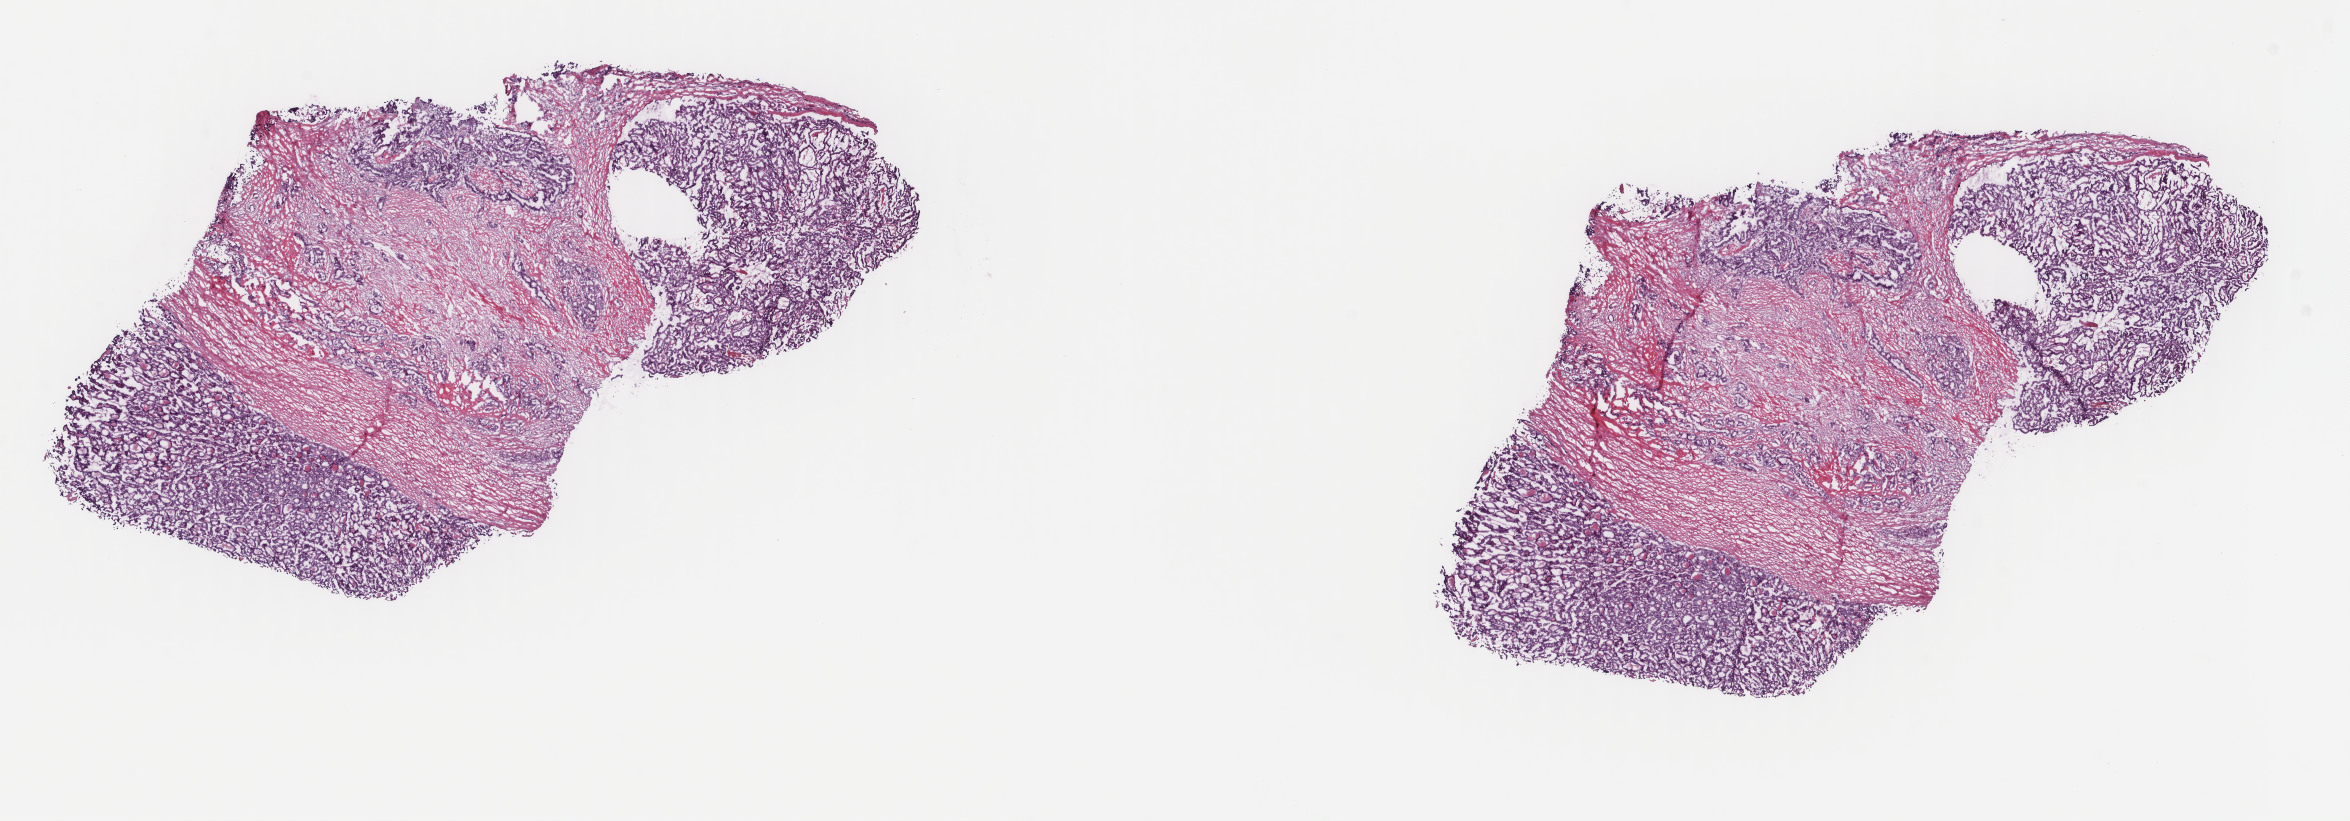
H&E-stained whole-slide image — low-resolution overview of the scanned area, about 18.7 x 6.5 mm; frozen section; sample: primary tumour, thyroid. Patient: female, age at initial diagnosis 19 years. Pathologist review of this section (percent, as recorded): tumour cells 90%, tumour nuclei 85%.
Diagnosis: Papillary adenocarcinoma, NOS (thyroid gland).